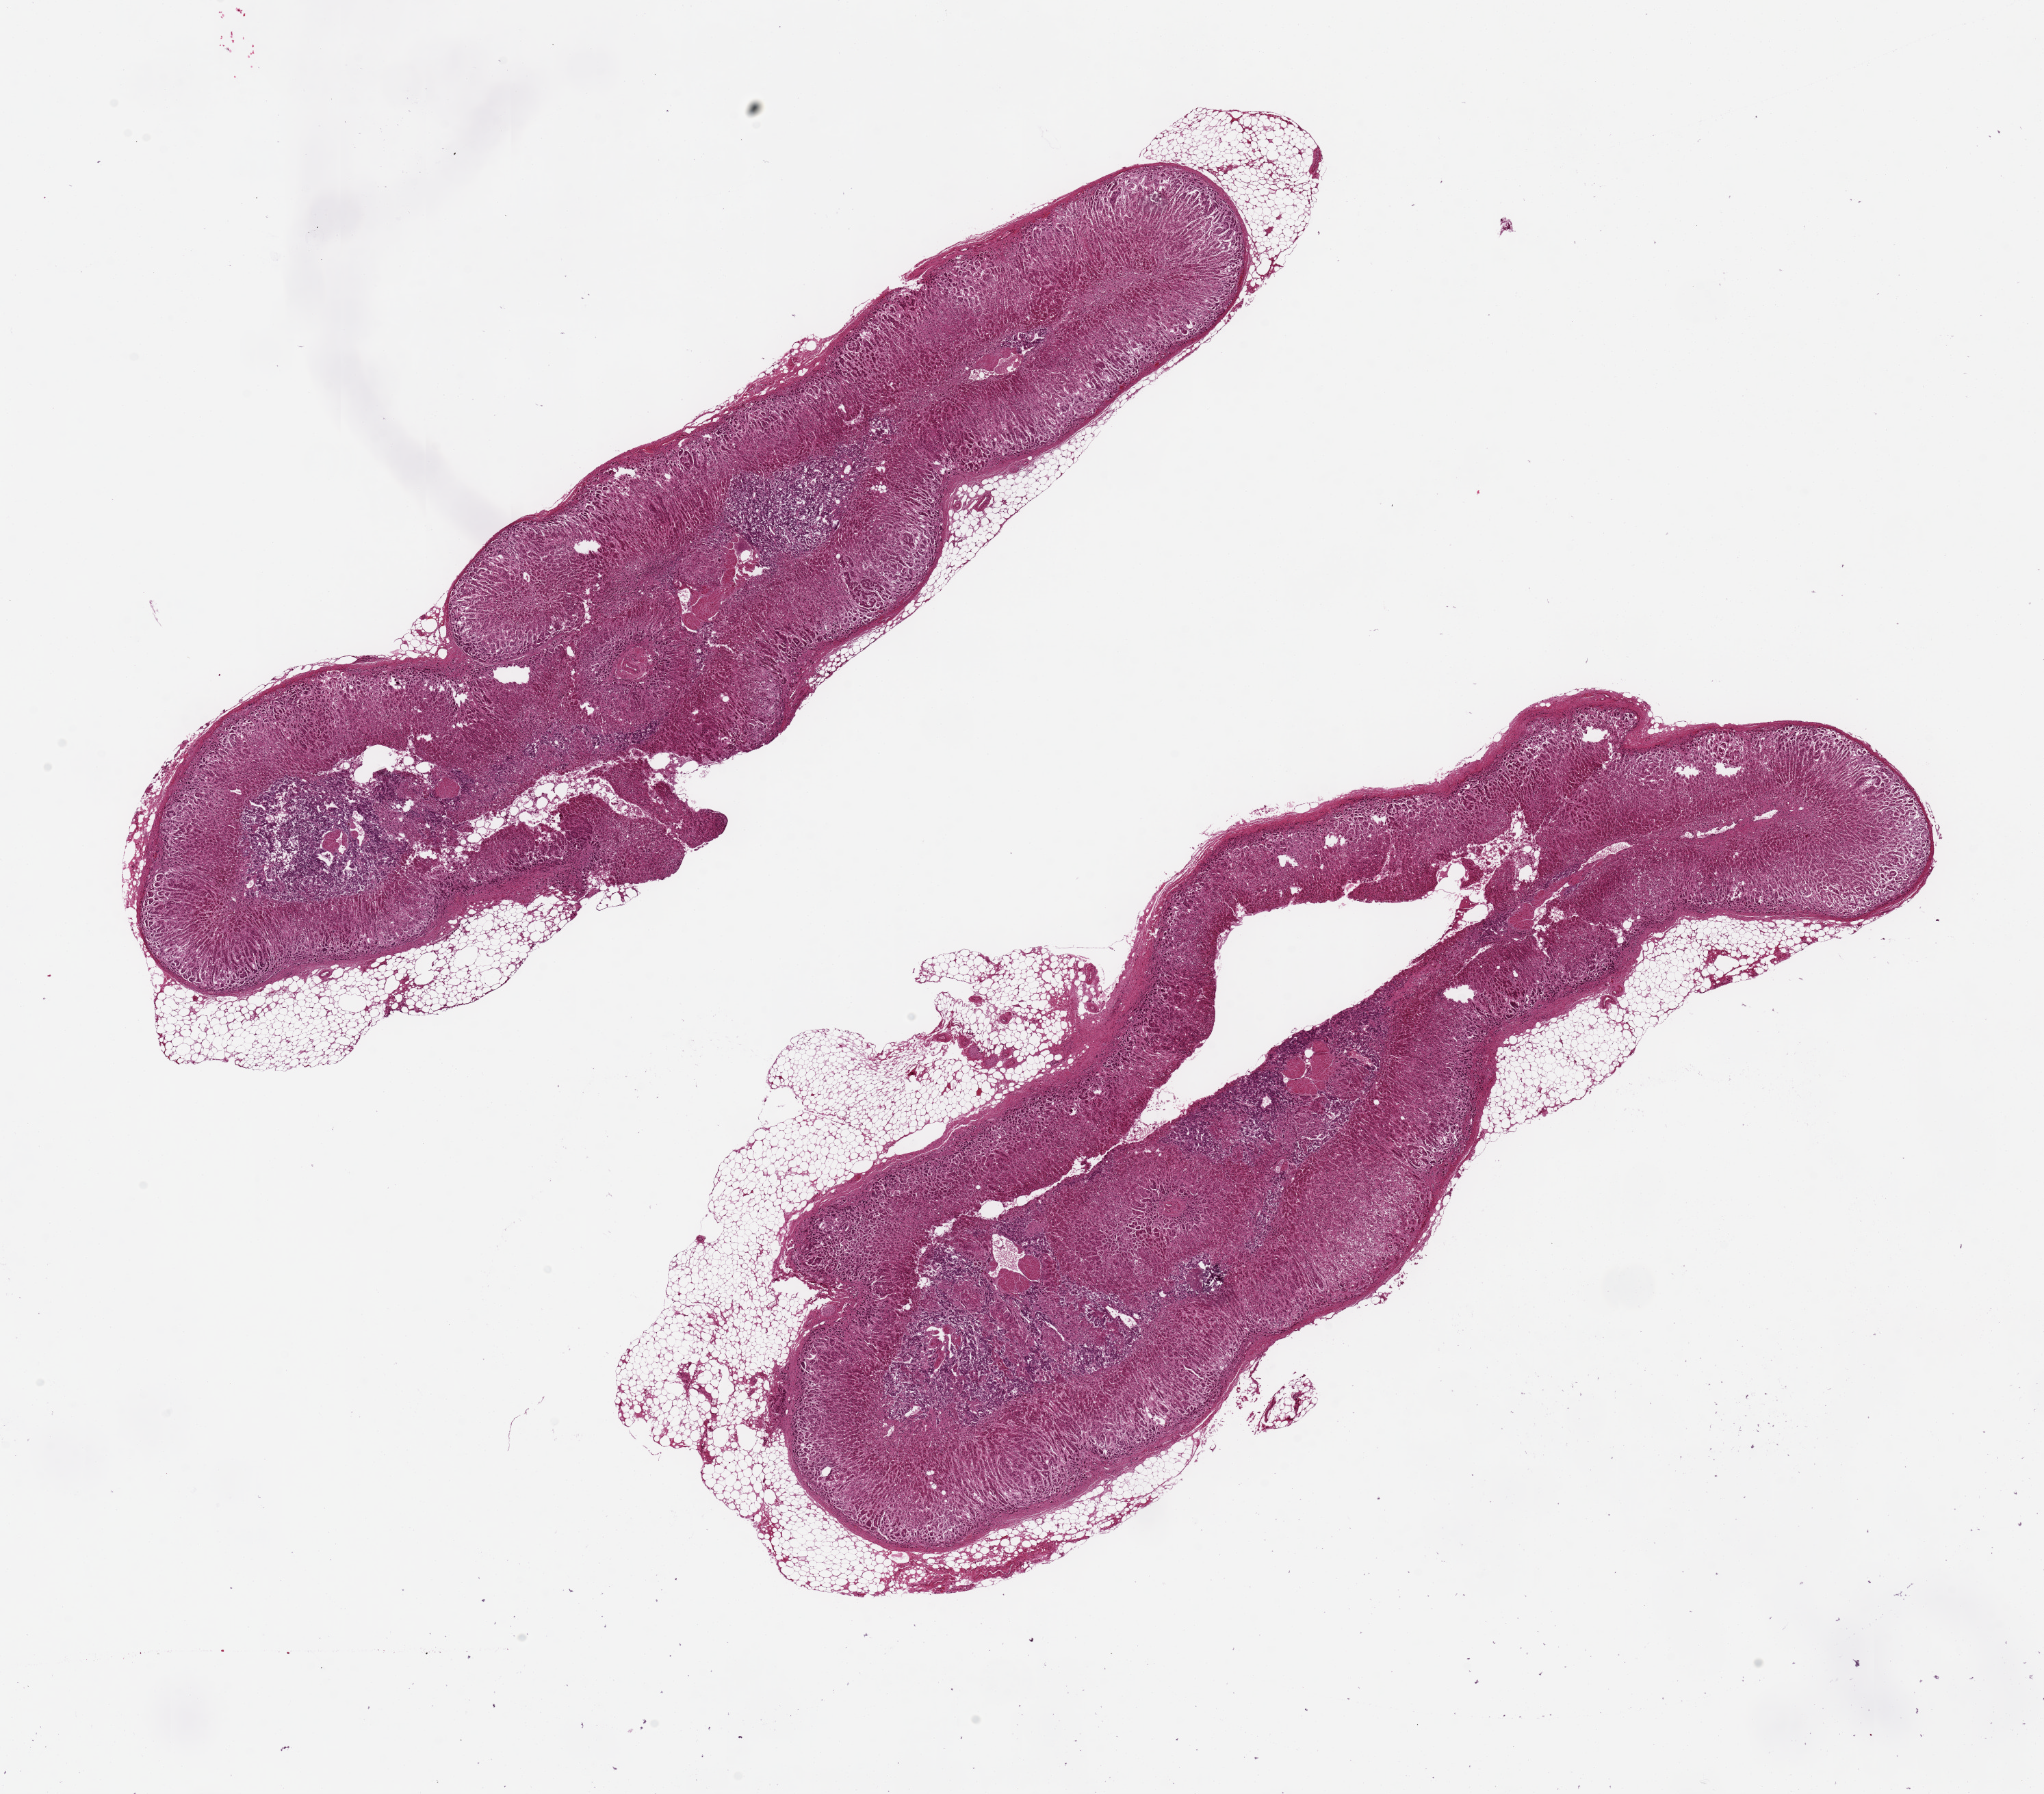
Digitized hematoxylin and eosin (H&E)-stained section — whole scanned area (about 23.6 x 20.7 mm, slide scanned at 20x) shown as a low-resolution overview. Donor: female.
Specimen: PAXgene-fixed paraffin-embedded (PFPE) section; section of adrenal gland (target tissue); donor tissue sample.